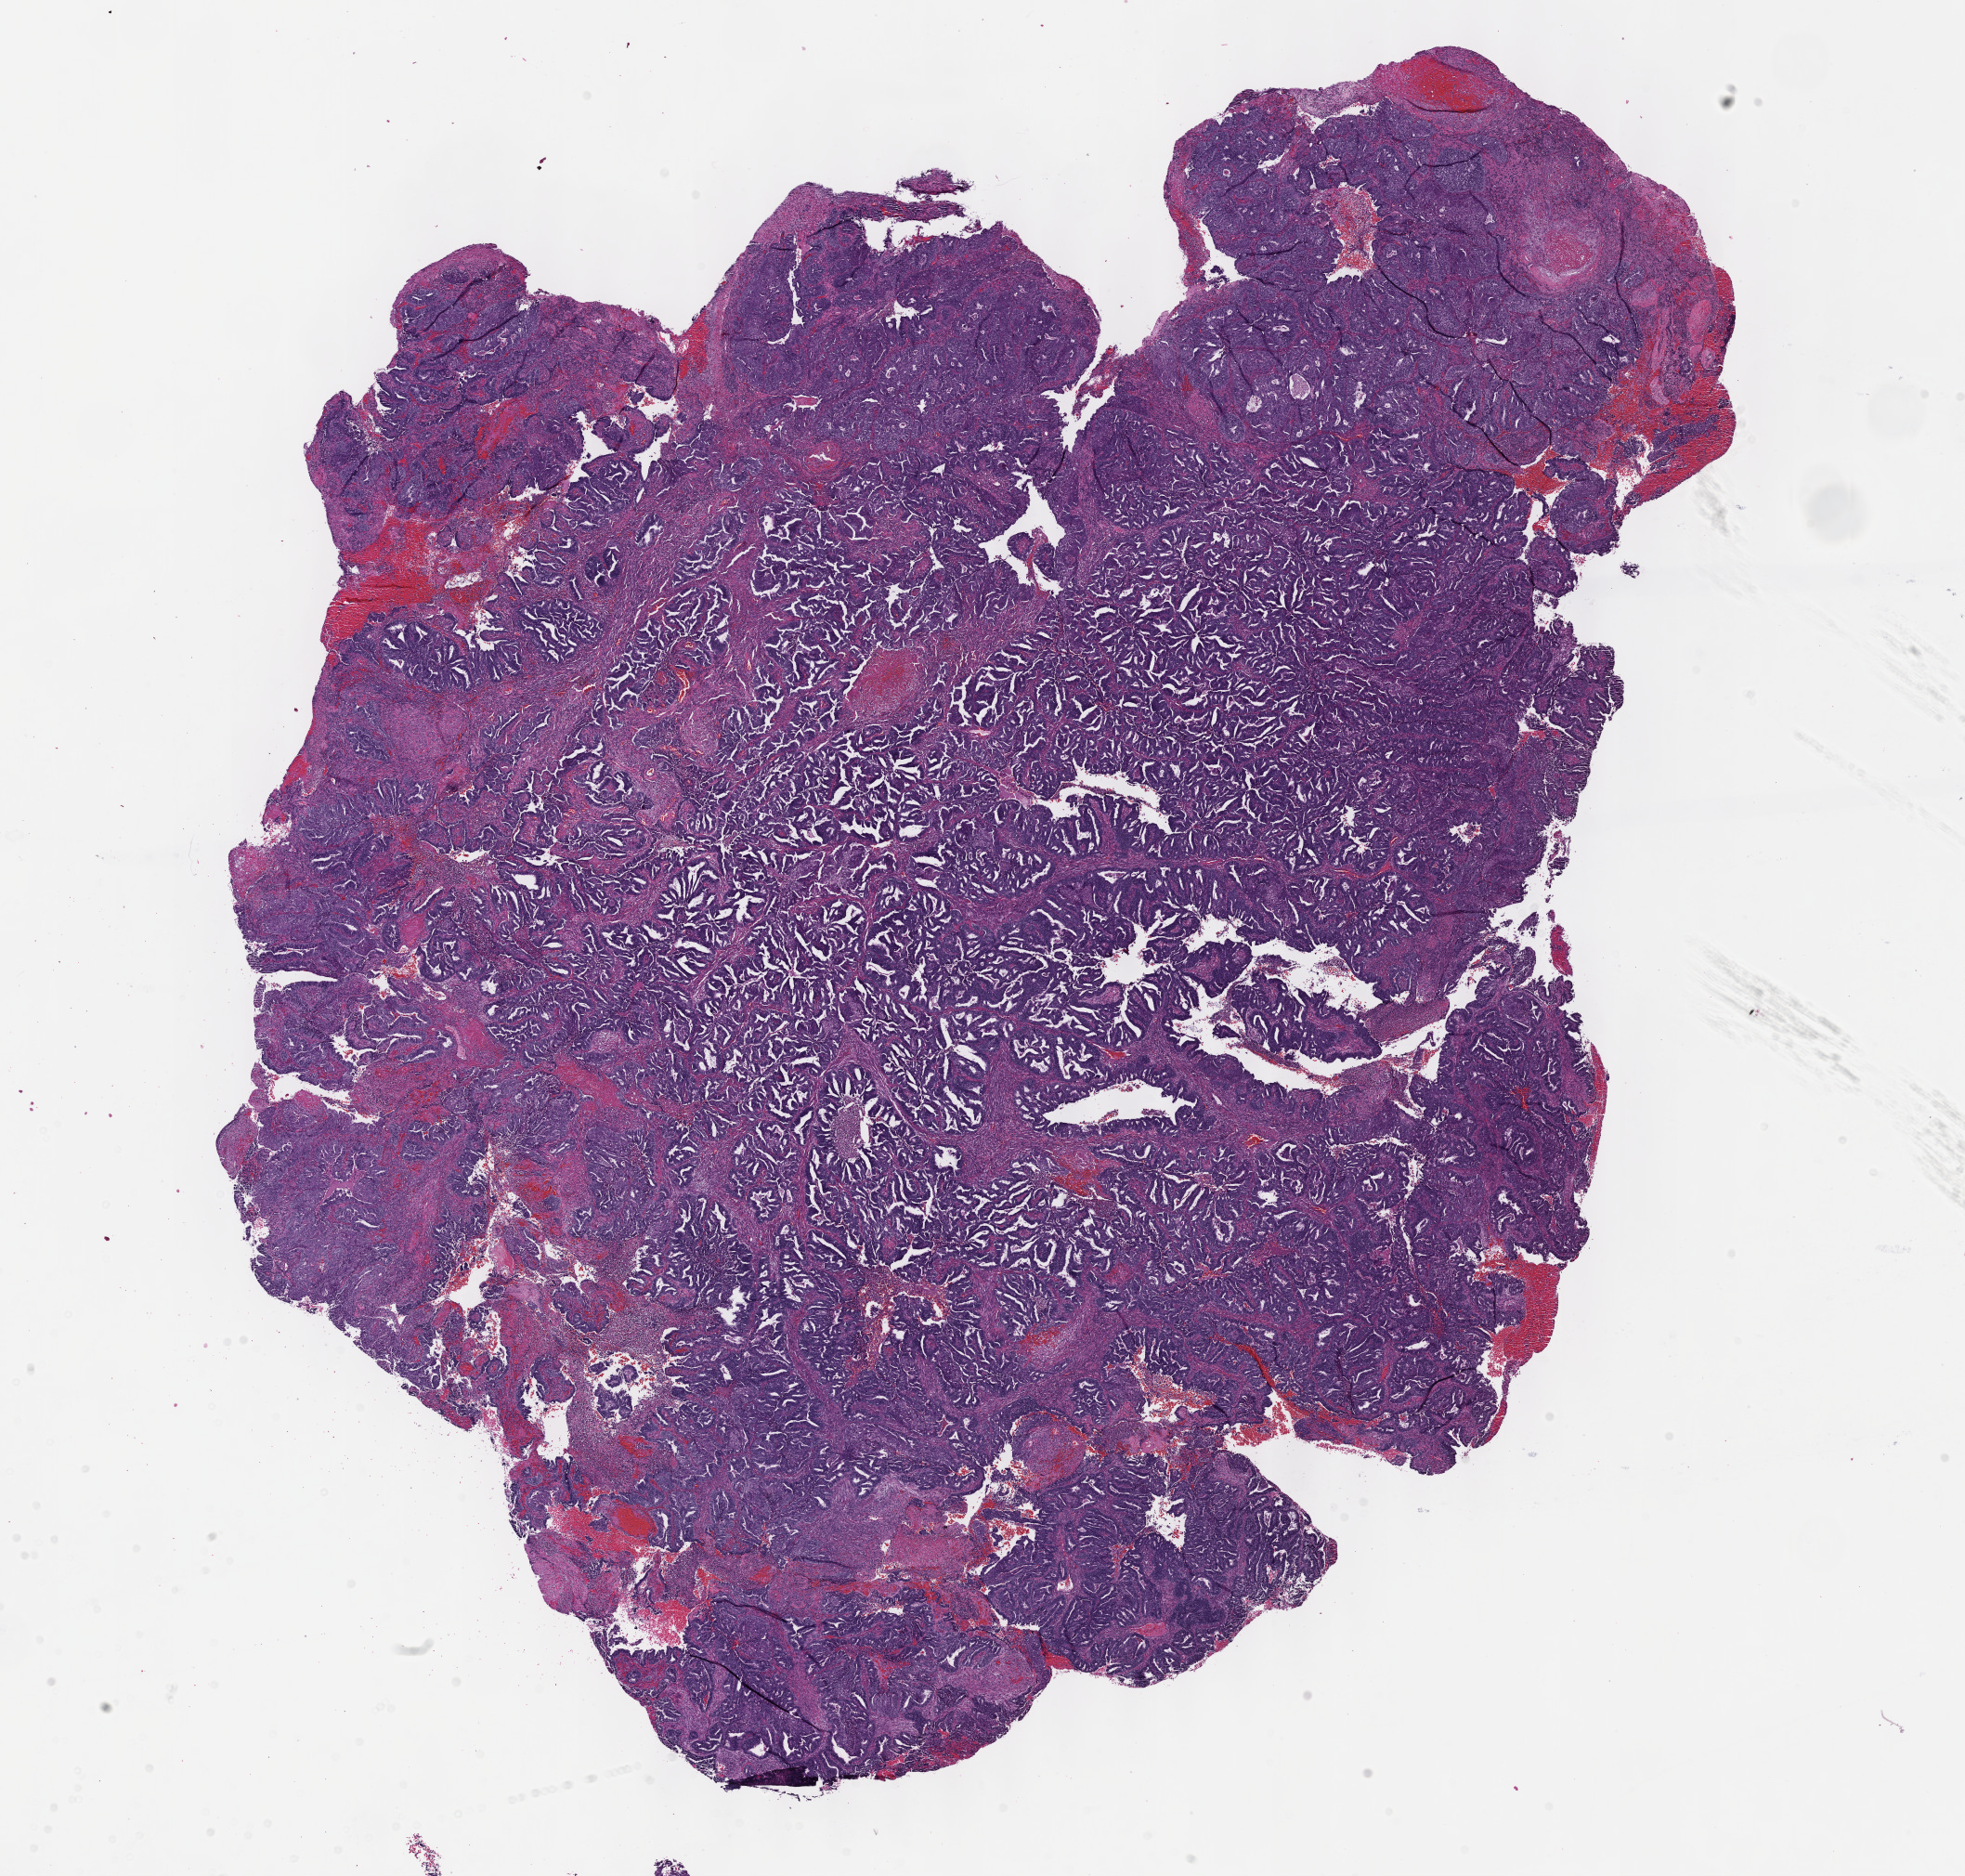
Whole-slide histology image, H&E, shown as a low-resolution overview of the whole scanned area (about 17.1 x 16.3 mm, slide scanned at 40x). FFPE section. Primary tumour sample from the uterus. Female patient; age at initial diagnosis 86 years. Histologic grade: G2 (moderately differentiated).
FIGO stage: IIIB. Histologic diagnosis: Endometrioid adenocarcinoma, NOS (isthmus uteri).